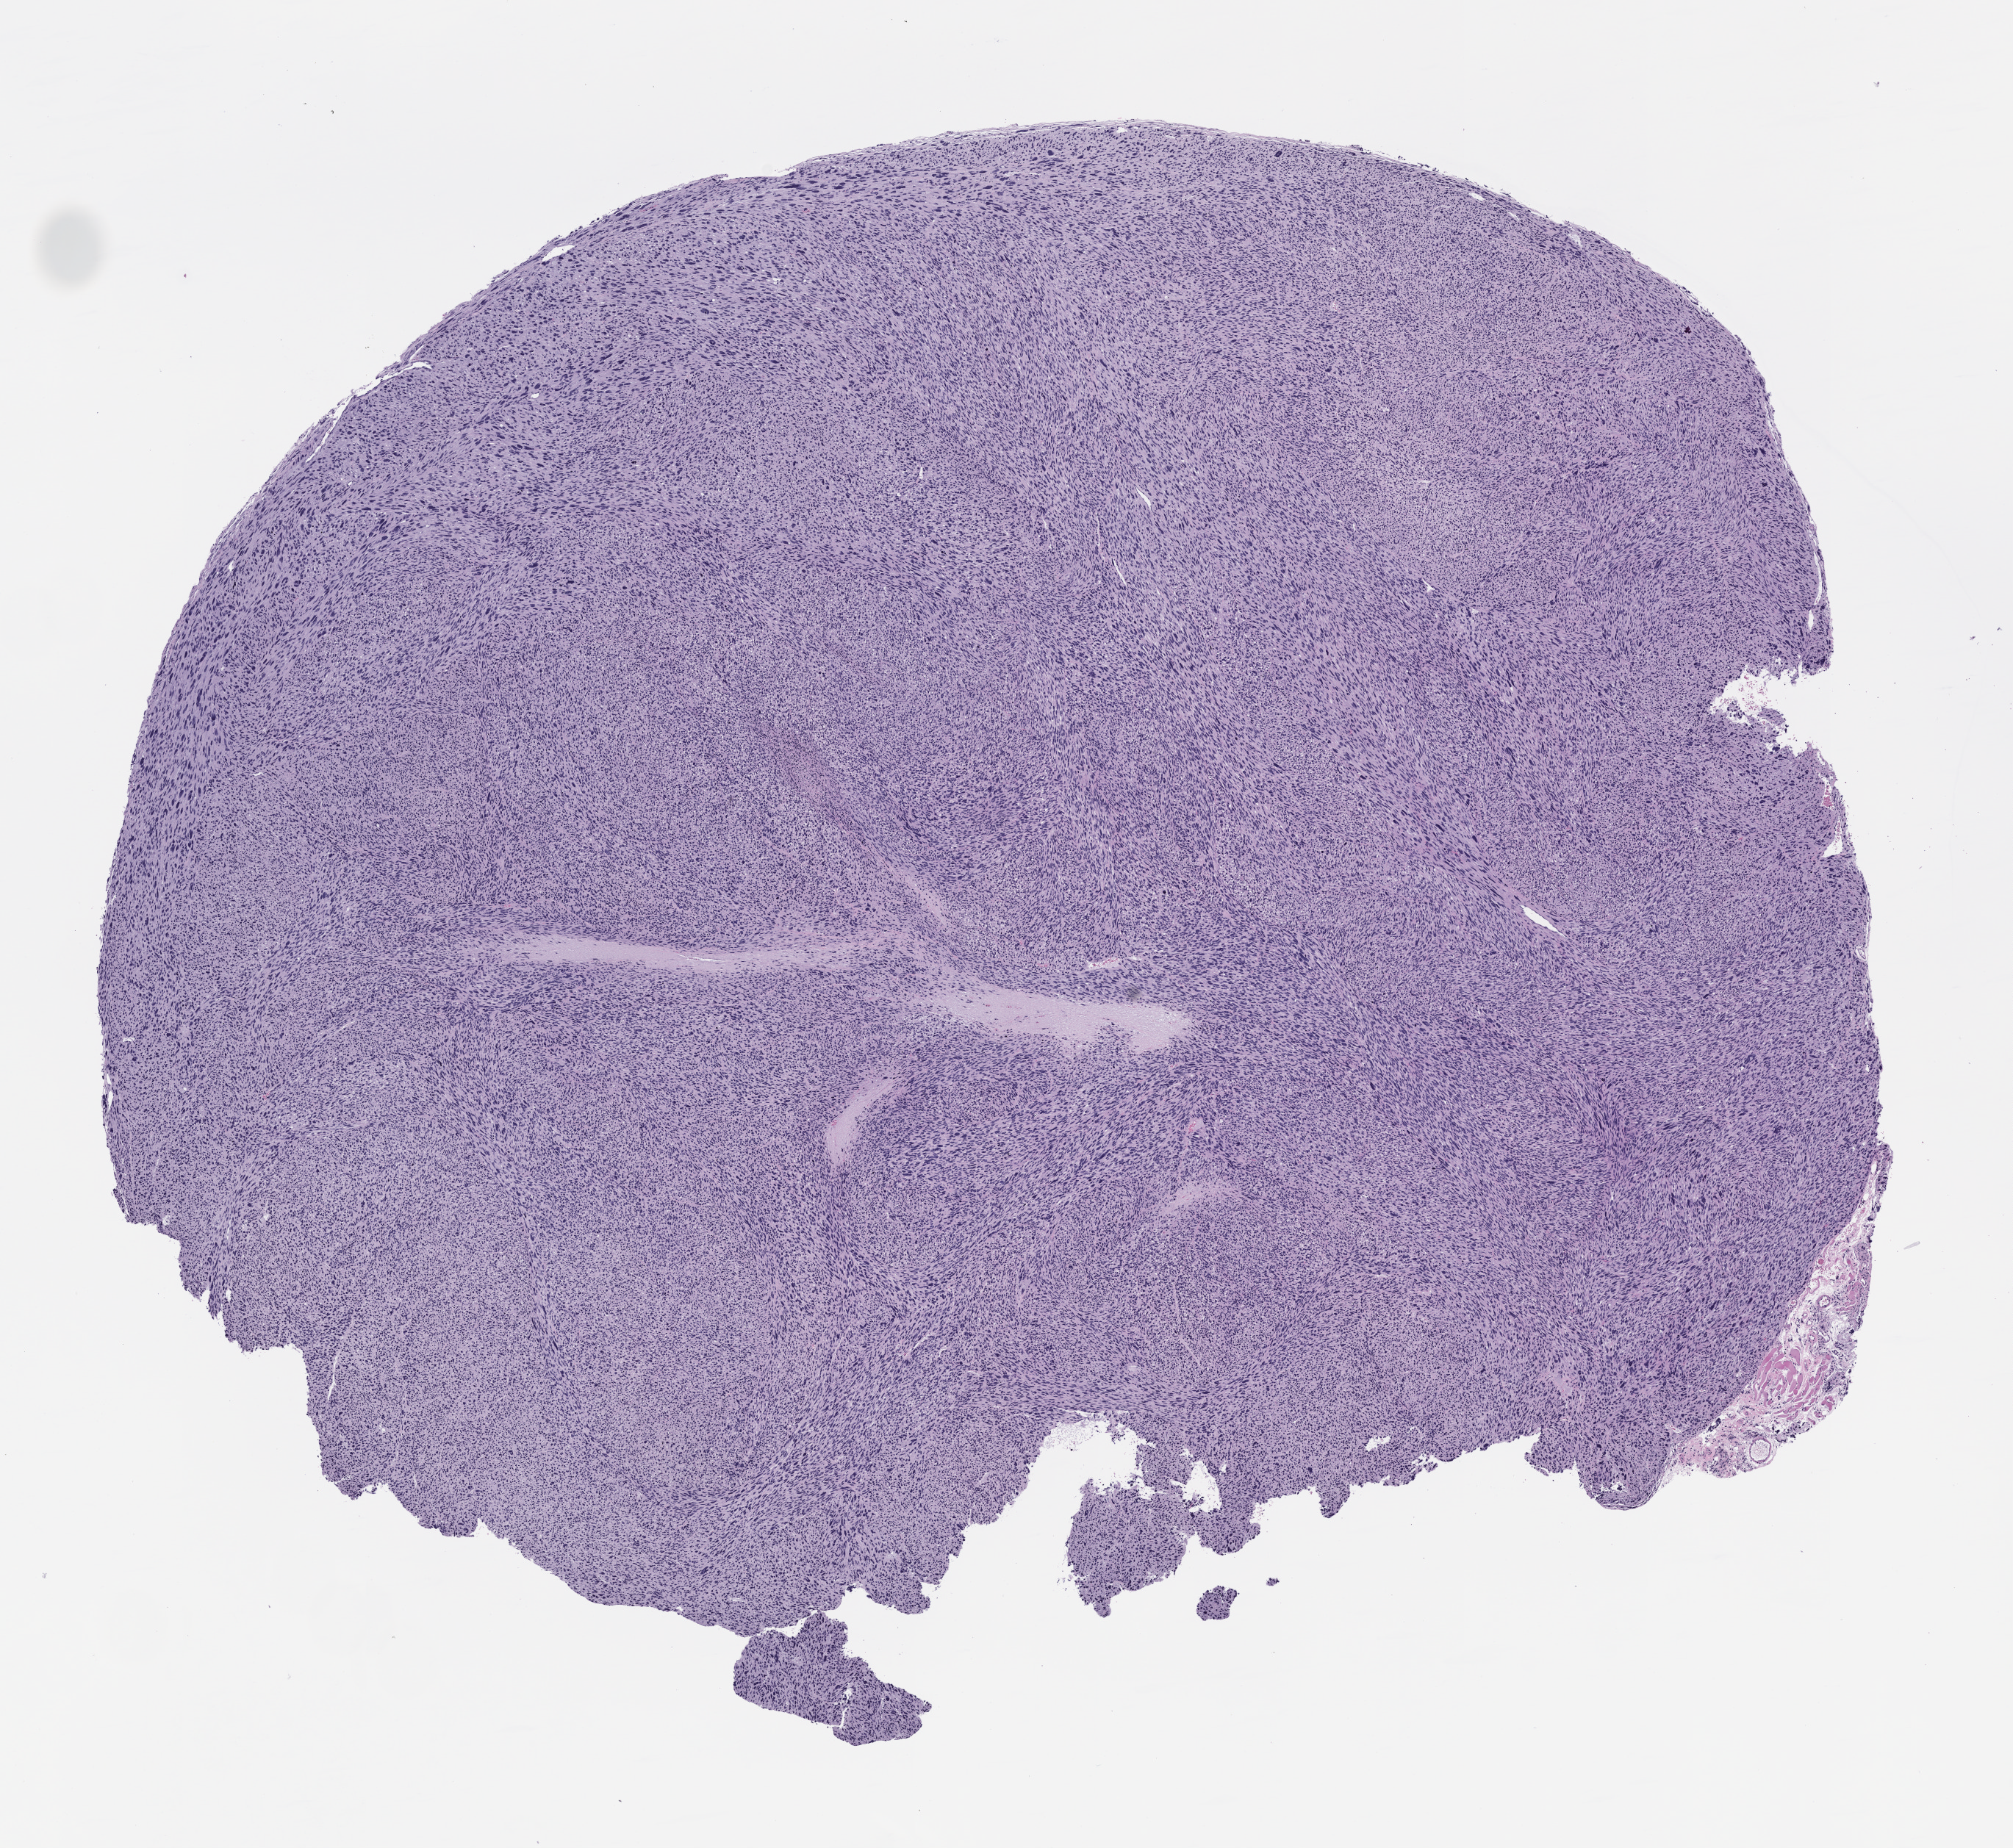
Whole-slide image, H&E: patient-derived xenograft (human tumor grown in a mouse), passage 1 — a low-resolution overview of the entire scanned area, about 11.0 x 10.1 mm. Formalin-fixed, paraffin-embedded (FFPE) tissue. Tumor site category: musculoskeletal.
Originating patient diagnosis: Leiomyosarcoma.